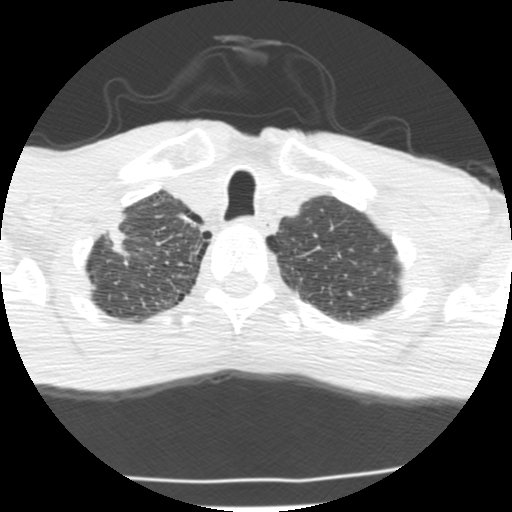
Chest CT (low-dose screening protocol), one axial image; second annual screen; lung window (W 1500 / L -600 HU); 2.5 mm slice thickness. Male, age 62 years at enrolment.
- Lesion marked by an expert reader, bounding box <79,212,144,274> (left, top, right, bottom; pixels).
- Screening reader's record for this exam (one nodule recorded; not confirmed to be the boxed lesion): non-calcified nodule or mass ≥4 mm, right upper lobe, 23 × 11 mm, spiculated (stellate) margins, soft tissue attenuation, pre-existing on the prior screen: yes.
- Lung cancer was diagnosed 277 days after this screen: adenocarcinoma, NOS, right upper lobe, poorly differentiated (G3), stage IIA (AJCC 6th edition), 22 mm at pathology.